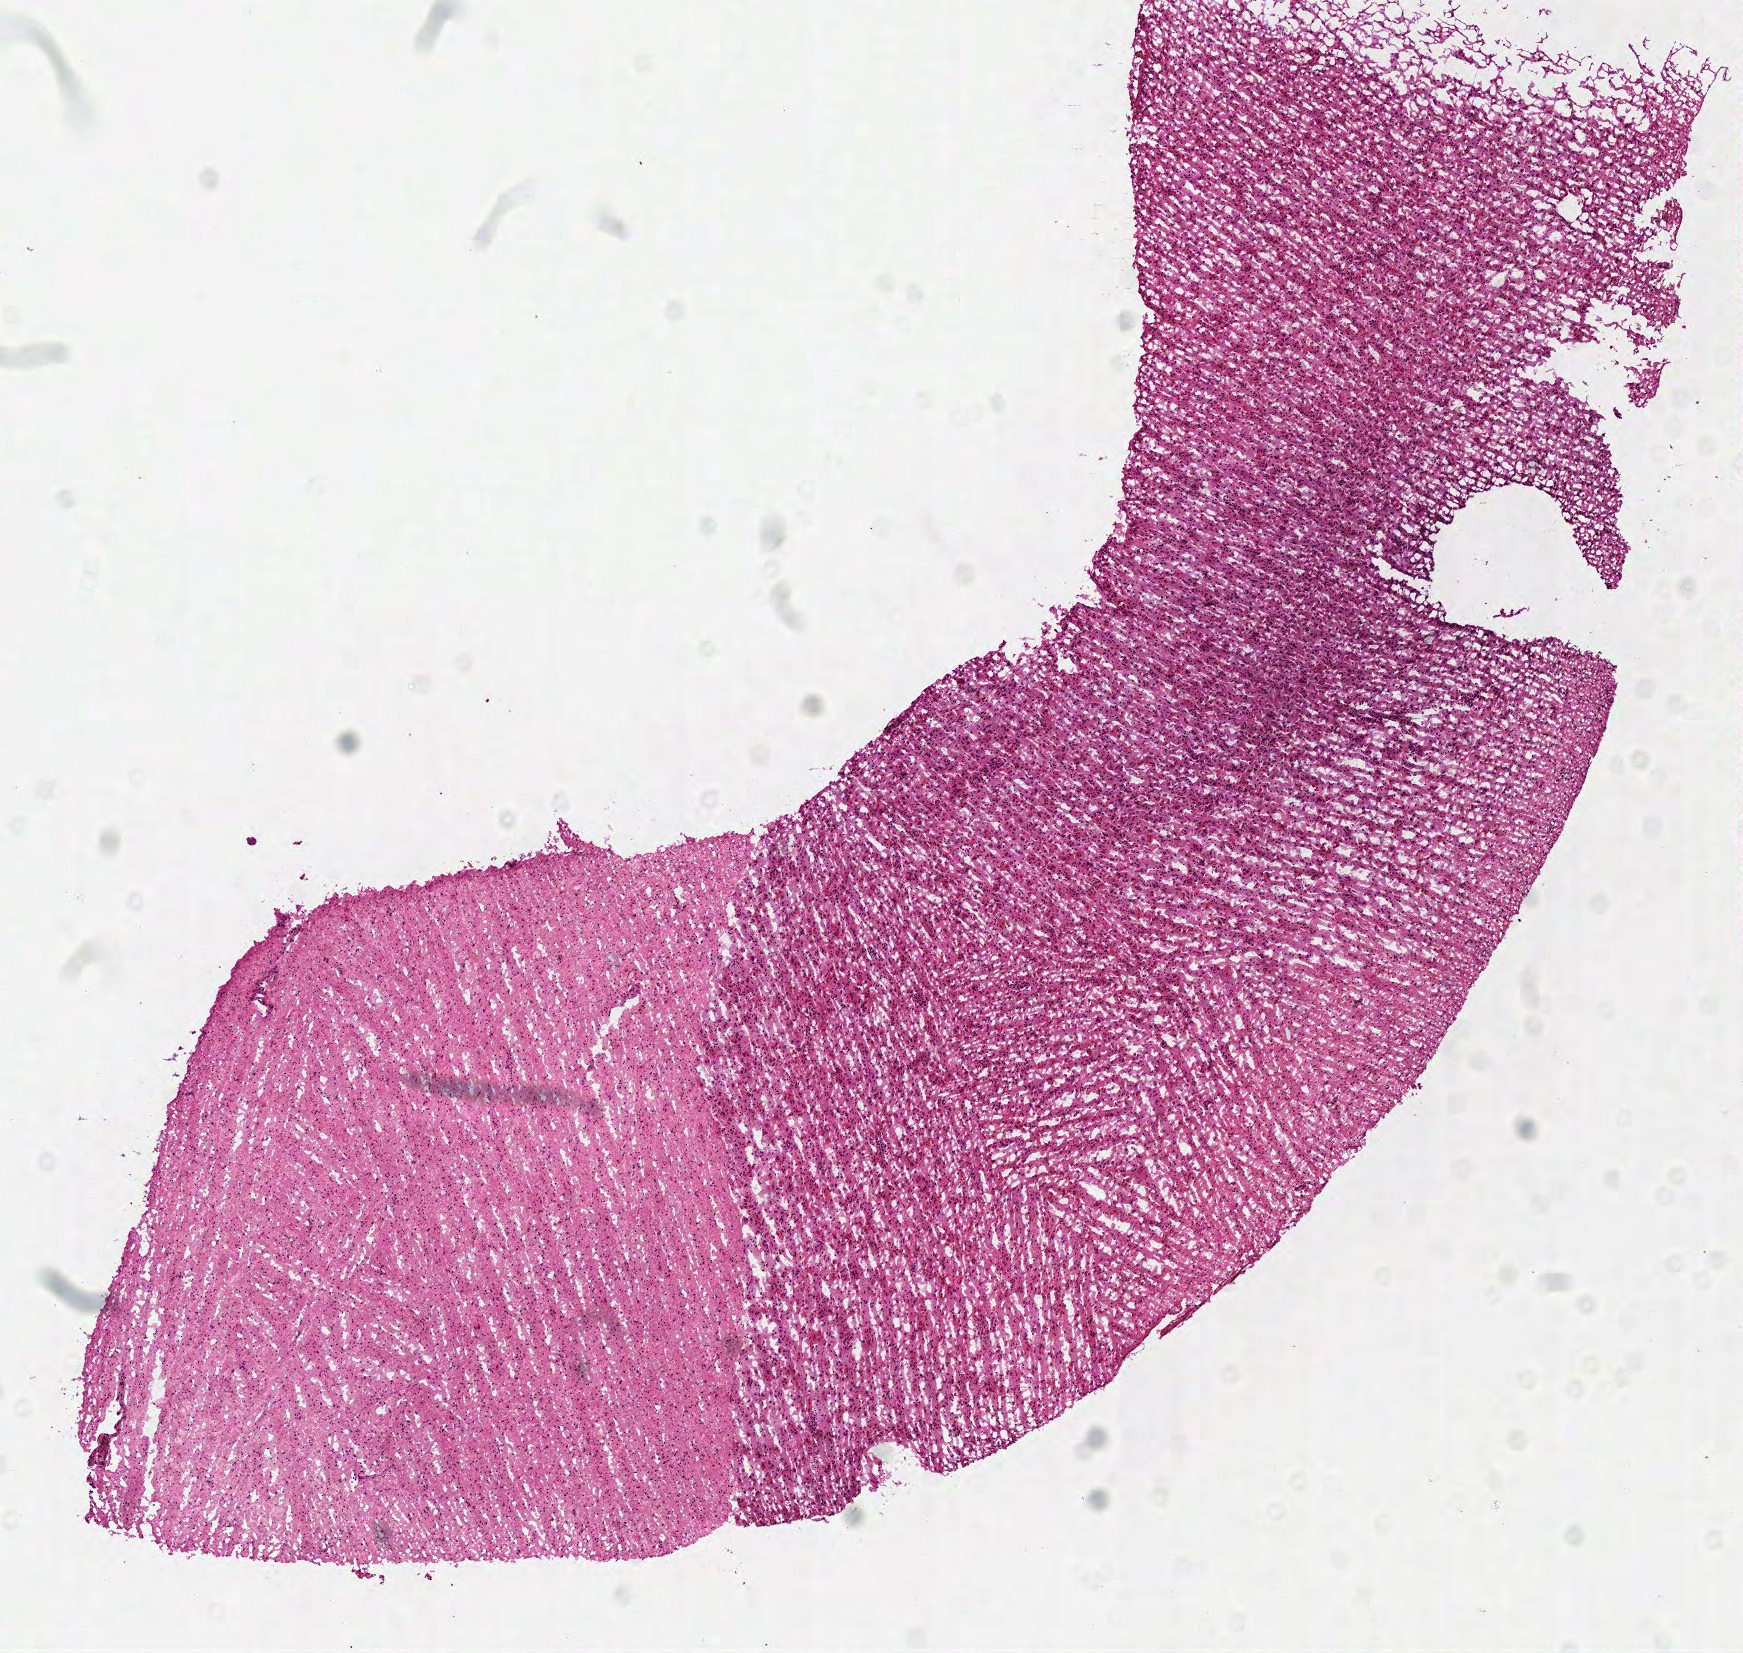
Digitized H&E tissue section (whole slide) — a low-resolution overview of the entire scanned area, about 6.9 x 6.5 mm (from a 40x scan), frozen section, brain, primary tumour sample. Patient: female, age at initial diagnosis 59 years. Histologic grade: G3 (poorly differentiated). Slide review estimates, as recorded: tumour cells 100%, tumour nuclei 75%, normal cells 0%, stromal cells 0%, necrosis 0%.
Diagnosis: Astrocytoma, anaplastic (cerebrum).